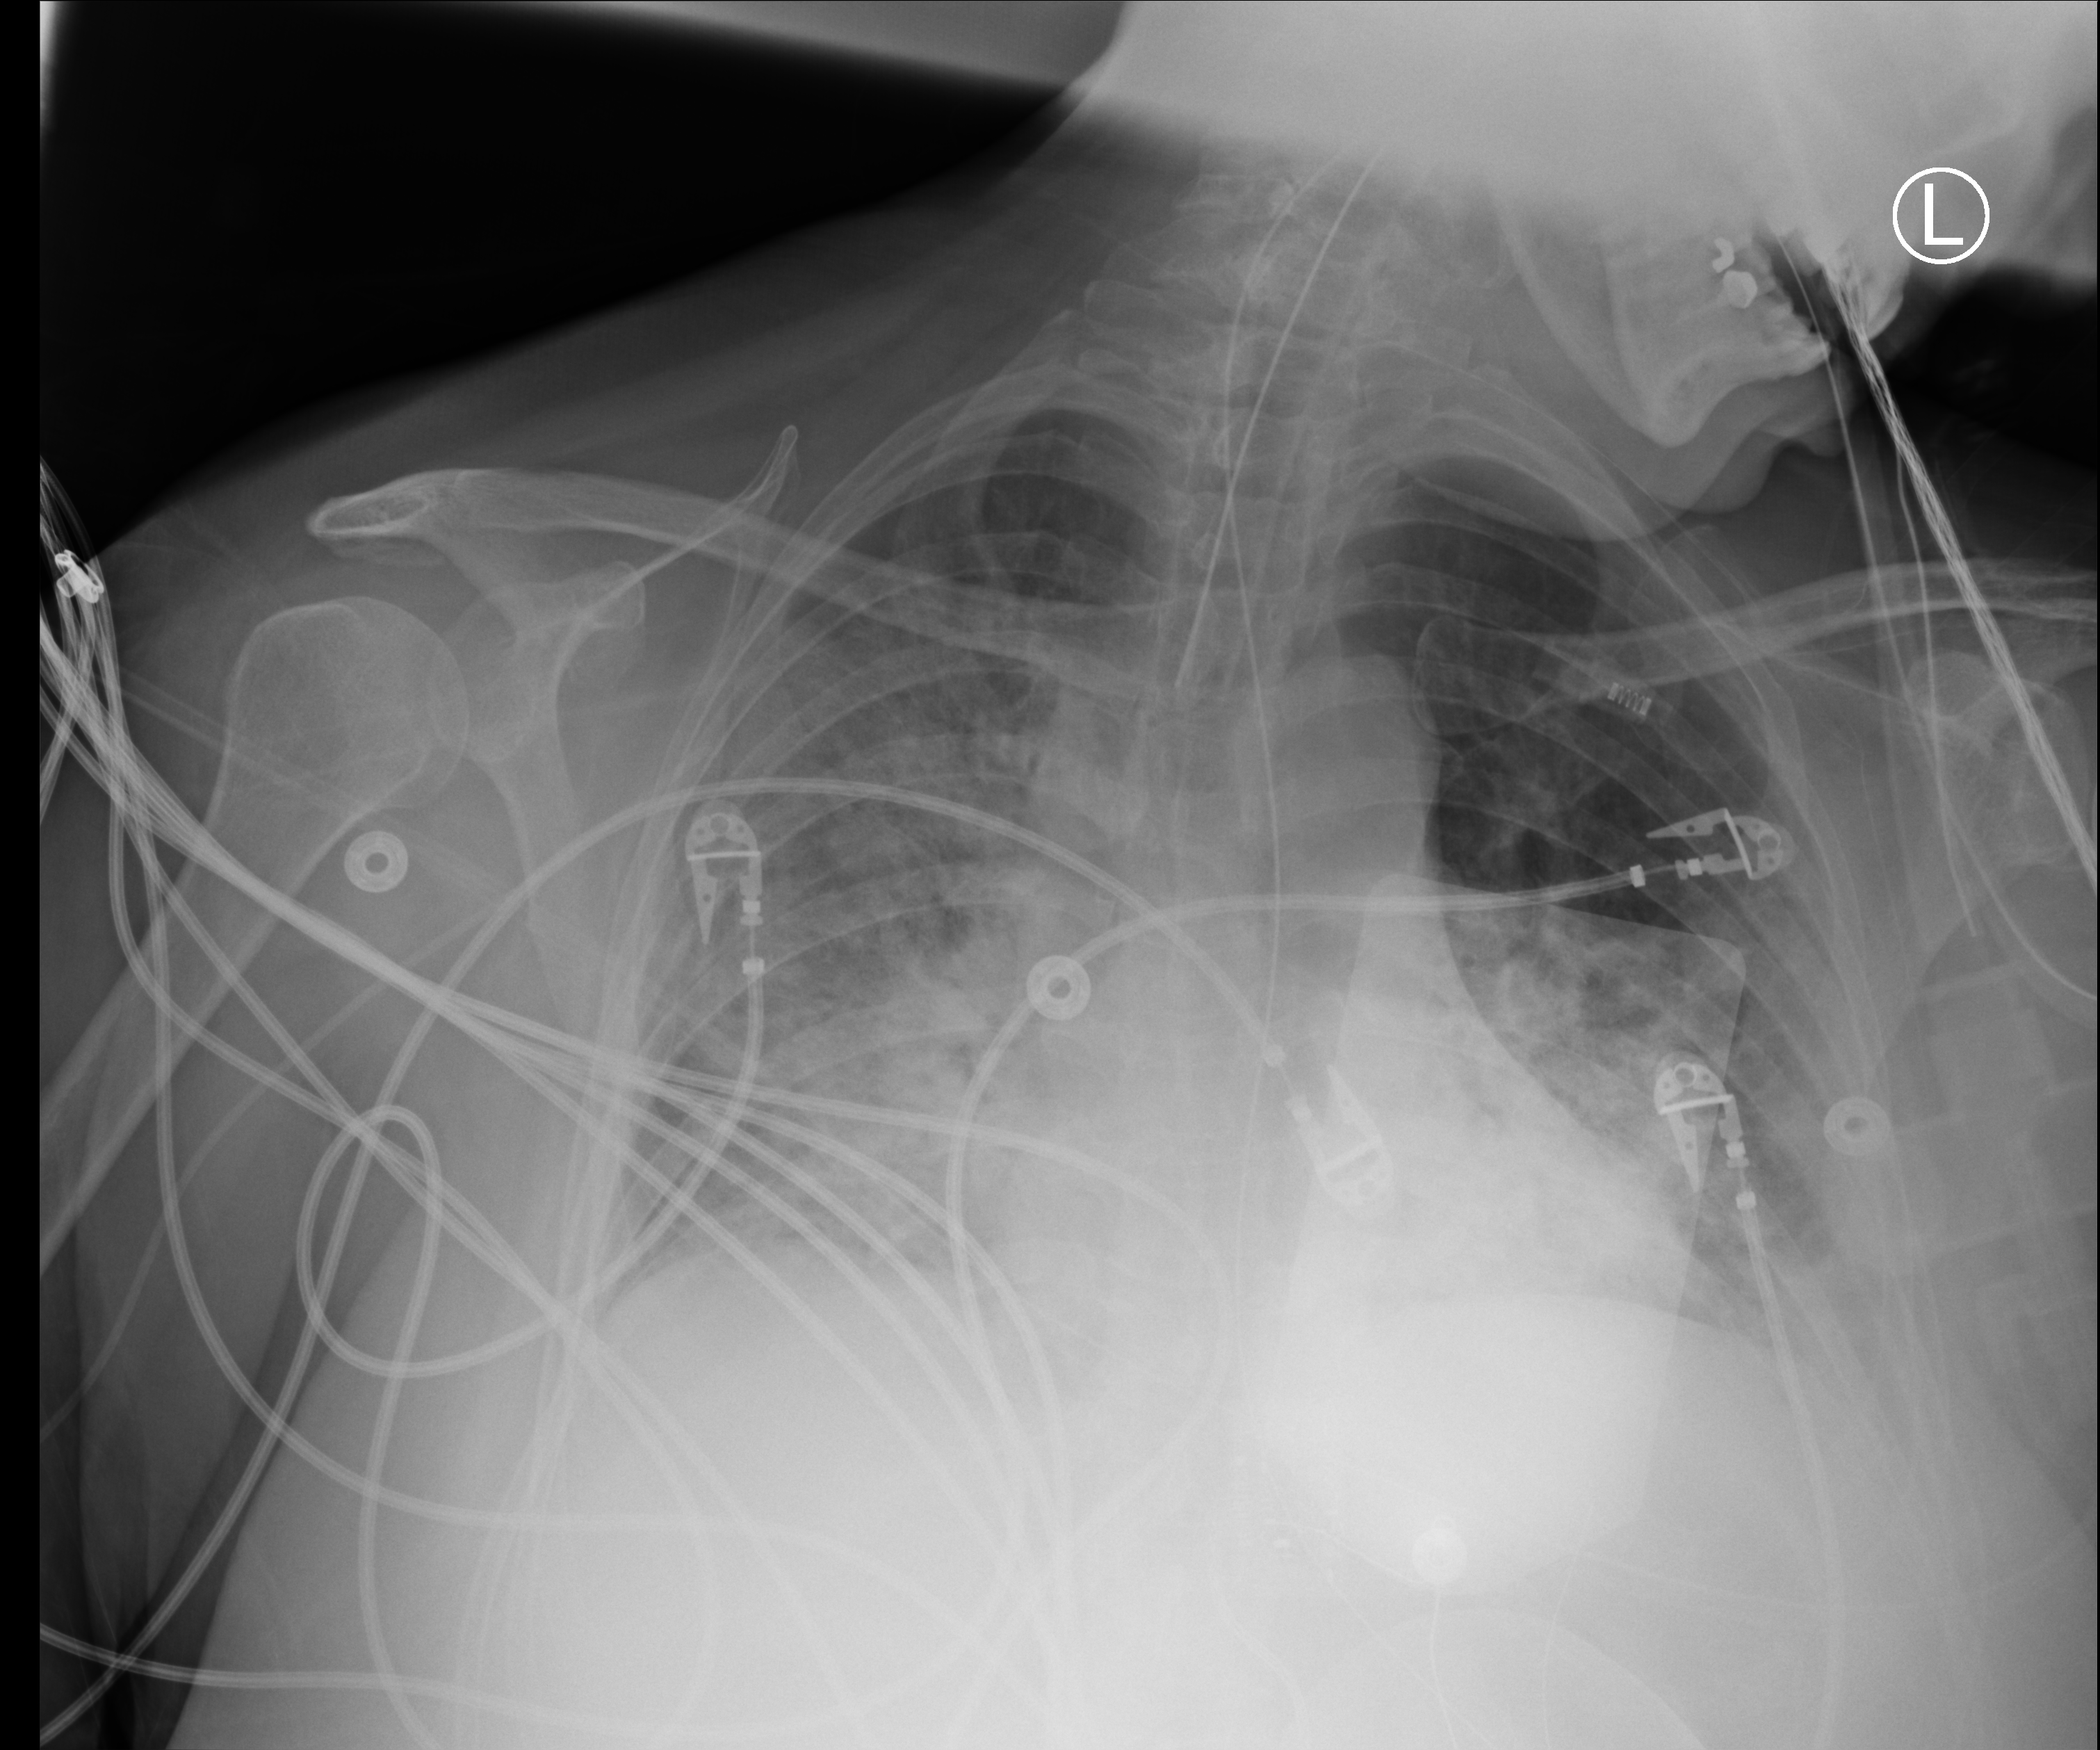
Portable chest radiograph, anteroposterior (AP) projection. Female patient hospitalised with COVID-19, age 18–59 years.
From the hospital-stay record, not from the radiograph (when in the stay this image was taken is not recorded): chronic kidney disease (admission record): no; COPD (admission record): no.